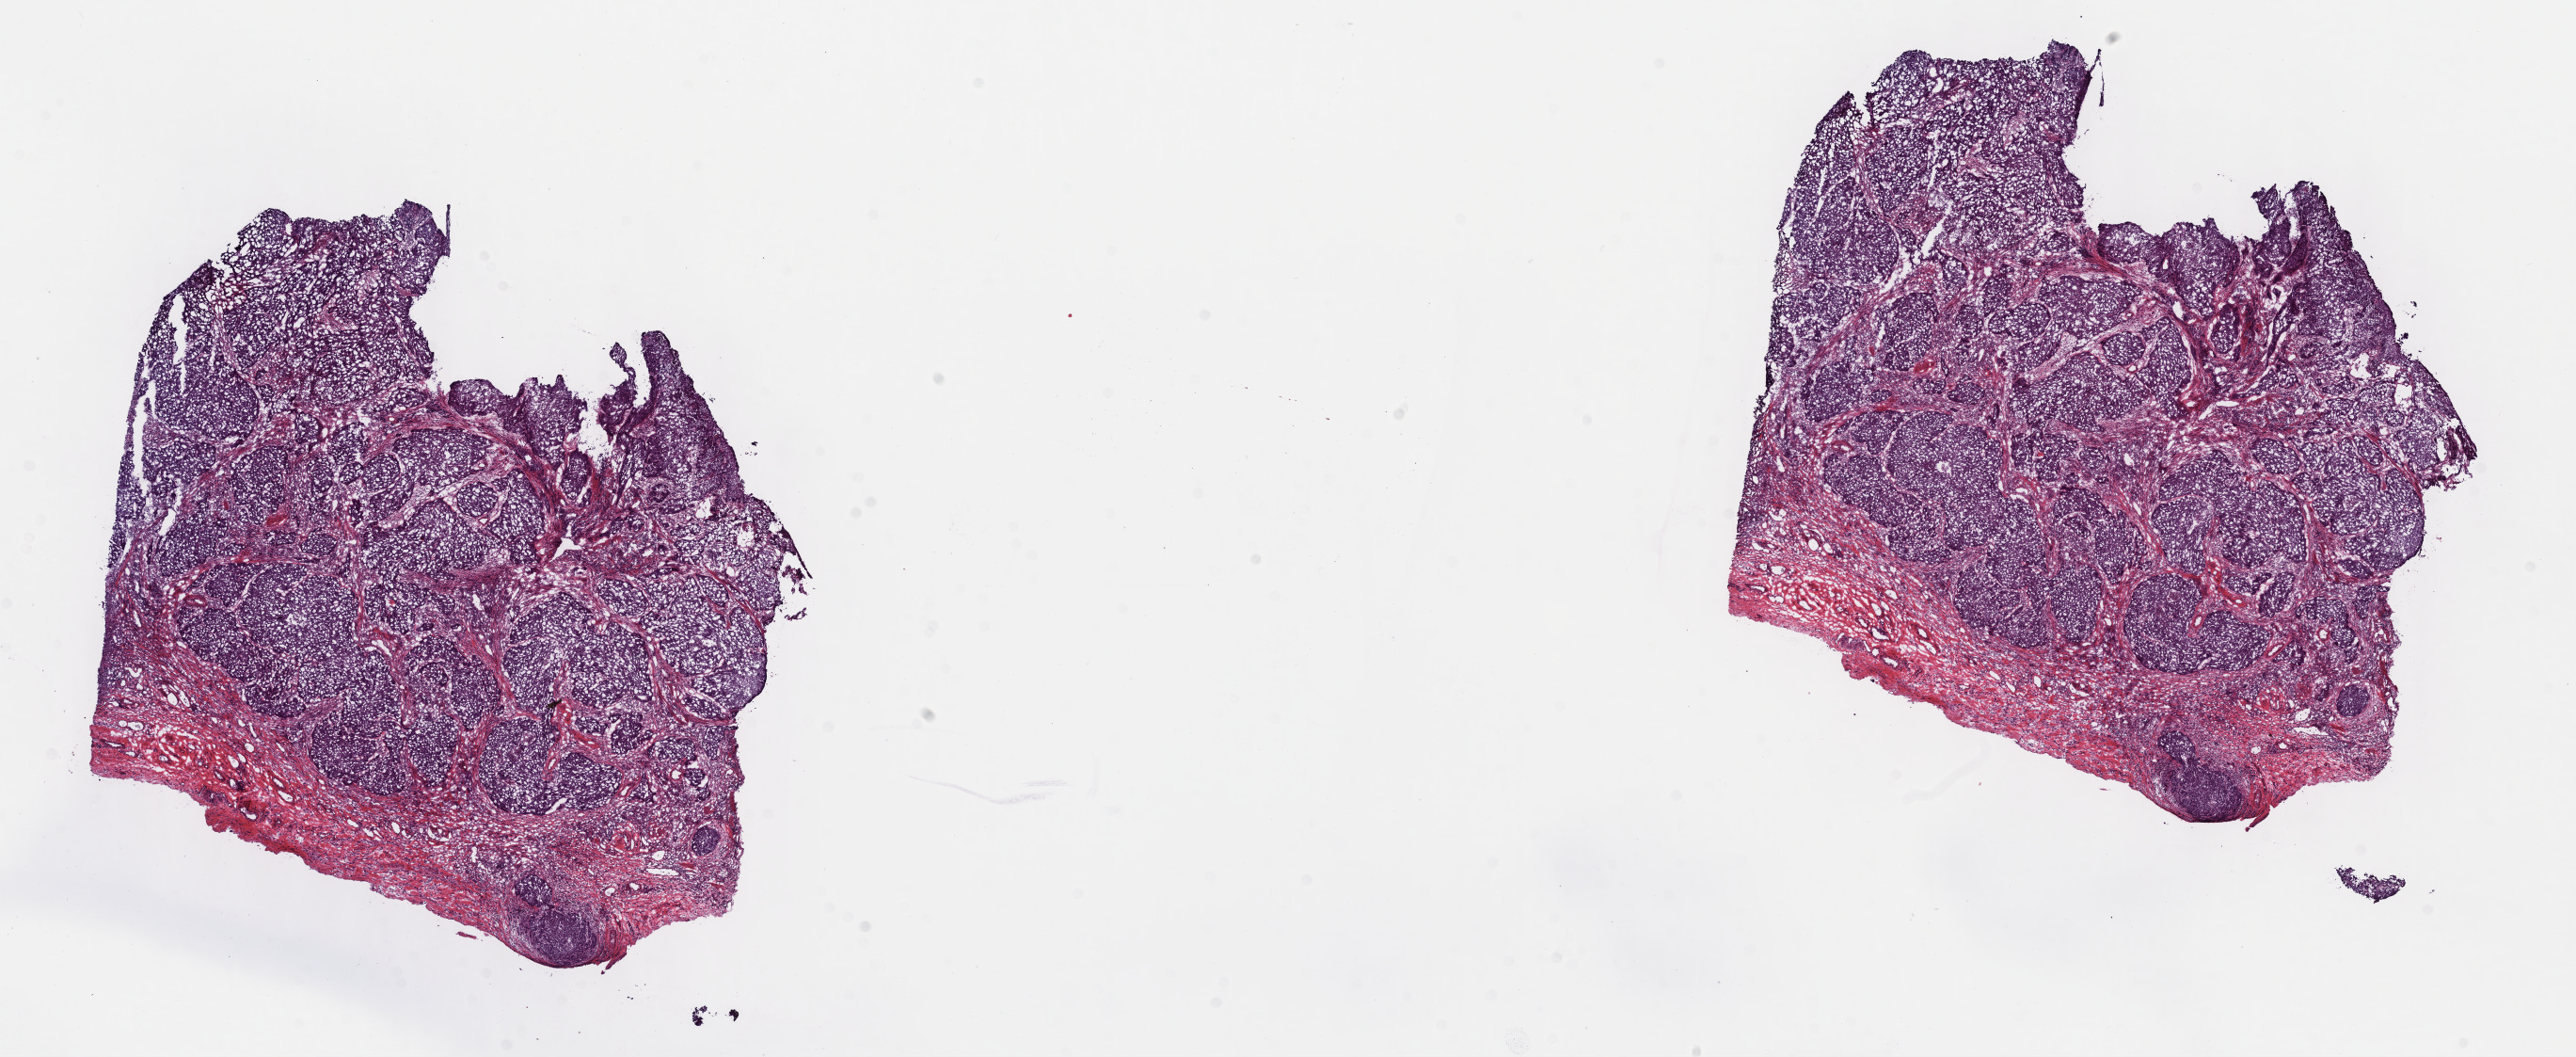
Whole-slide histology image, H&E-stained, low-resolution overview of the scanned area, about 22.1 x 9.1 mm (acquisition: 40x scan); frozen section from the top of the tissue portion; sample: primary tumour, bladder. Female, age 61 years at initial diagnosis. Histologic grade: high grade. Composition of this section per pathologist review: tumour cells 85%, tumour nuclei 70%, normal cells 15%, stromal cells 0%, necrosis 0%. Inflammatory infiltration, as recorded: lymphocyte infiltration 3%, monocyte infiltration 0%, neutrophil infiltration 0%.
AJCC pathologic stage: IV (7th edition). Lymph nodes positive (case pathology): 1 of 22 examined. Pathologic diagnosis: Transitional cell carcinoma (posterior wall of bladder).